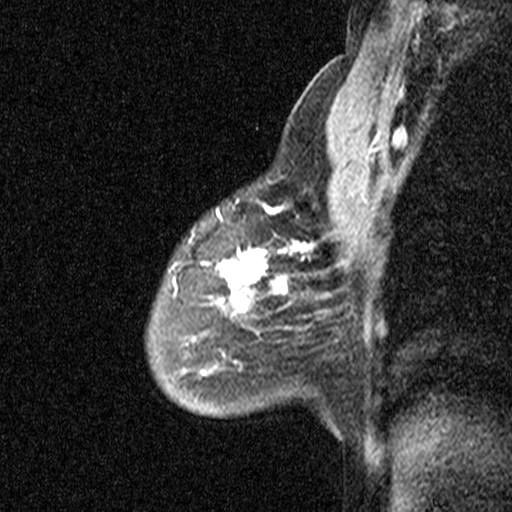
Breast MRI (dynamic contrast-enhanced), one sagittal slice; slice 33 of 44 in the series (ordered by position); dynamic contrast-enhanced study with each time point stored as its own series, time point 2 of 3 at this slice position (early post-contrast, ordered by acquisition time); 1.5 T; TE 4.5 ms, TR 11 ms; 512 × 512 image matrix. Female patient, age 53 years. From the clinical record (not read from this slice): setting: breast cancer imaged before/during neoadjuvant chemotherapy; receptor status: HR-positive, HER2-negative.
Structures marked on this image (semi-automatic segmentation, software-assisted and operator-edited):
- analysis volume of interest (the breast-tissue region the enhancement analysis was run in; not a lesion): box from (x=88, y=176) to (x=313, y=423) px
- tumour enhancement mask (voxels above the 90 % enhancement threshold inside the analysis volume of interest): (x=217, y=202)–(x=310, y=311)